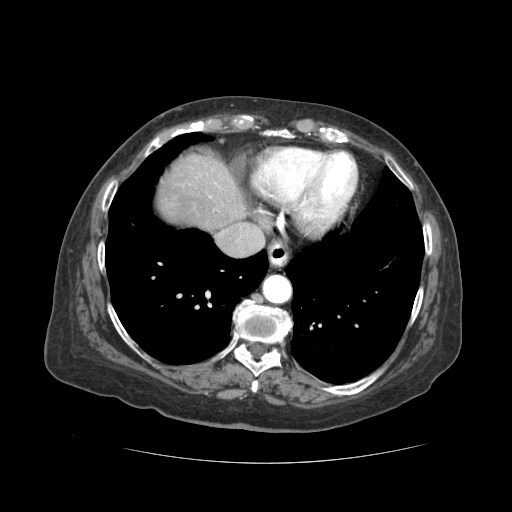
Contrast-enhanced abdominal CT (liver protocol), one axial slice. Slice 46 of 59 in the series (ordered by position). Reconstruction kernel STANDARD. Soft-tissue window (W 400 / L 40 HU). 2.5 mm slice thickness. 512 × 512 image matrix, field of view 380 × 380 mm. Case-level facts recorded for this patient, not image findings: diagnosis: hepatocellular carcinoma (patient treated with transarterial chemoembolisation; whether this scan precedes or follows treatment is not stated here); TNM stage (as recorded): Stage-I; Child-Pugh class: A; tumour nodularity: uninodular.
Annotated regions visible in this slice (semi-automatically segmented with operator editing):
- liver parenchyma outside the tumour (the mass and vessels are separate outlines, so this box may not span the whole liver): bounding box [x1, y1, x2, y2] px = [158, 154, 246, 228]